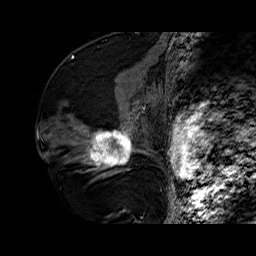
Breast MRI (dynamic contrast-enhanced), one sagittal slice. Position 32 of 60 along the scan axis. Dynamic contrast-enhanced series, time point 2 of 6 at this slice position (early post-contrast). 1.5 T. TE 6.4 ms, TR 32.7 ms. 256 × 256 image matrix. Female patient. From the clinical record (not read from this slice): setting: breast cancer imaged before/during neoadjuvant chemotherapy; receptor status: HR-positive, HER2-negative.
Structures marked on this image (semi-automatically segmented with operator editing):
- analysis volume of interest (the breast-tissue region the enhancement analysis was run in; not a lesion): bounding box (x1, y1, x2, y2) in pixels: (73, 110, 141, 178)
- tumour enhancement mask (voxels above the 100 % enhancement threshold inside the analysis volume of interest): (86, 131, 134, 168)